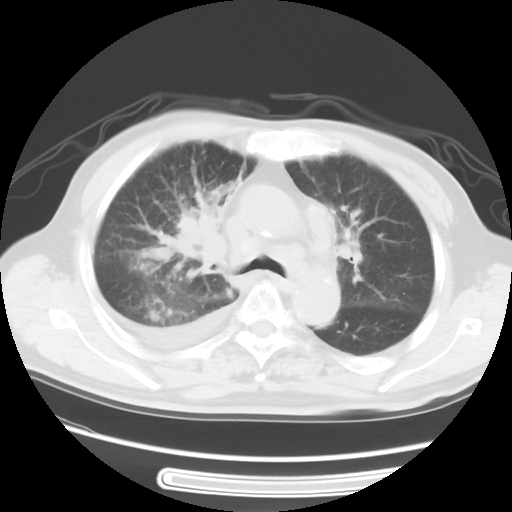
Chest CT, one axial slice. Slice 37 of 56 in the series (ordered by position). 120 kVp. Lung window (W 1500 / L -600 HU). 5 mm slice thickness. 512 × 512 image matrix. Male patient, age 77 years. From the clinical record (not read from this slice): clinical TNM (as recorded): T3 N3 M1b; histopathological grade: G3.
Outlined on this slice (bounding box drawn by a radiologist):
- lung tumour (recorded histology: small cell carcinoma): bounding box (x1, y1, x2, y2) in pixels: (165, 200, 227, 273)